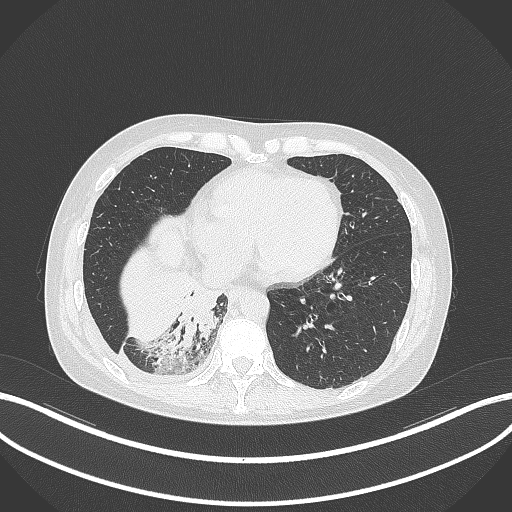
Chest CT, one axial slice; slice 94 of 329 in the series (ordered by position); reconstruction kernel B70f; 120 kVp; lung window (W 1500 / L -600 HU); 1 mm slice thickness; 512 × 512 image matrix, field of view 400 × 400 mm. Patient: female, 63 years. Case-level facts recorded for this patient, not image findings: clinical TNM (as recorded): T1c N0 M0.
Structures marked on this image (bounding box drawn by a radiologist):
- lung tumour (recorded histology: adenocarcinoma): box from (x=166, y=282) to (x=223, y=353) px